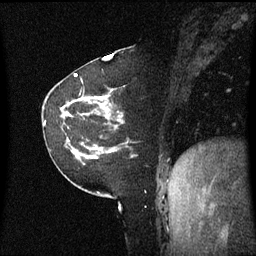
Breast MRI (dynamic contrast-enhanced), one sagittal slice; position 20 of 60 along the scan axis; dynamic contrast-enhanced series, image 2 of 3 at this slice position (ordered by acquisition); 1.5 T; TE 4.2 ms, TR 8.4 ms; 256 × 256 image matrix, field of view 220 × 220 mm. Female patient, age 60 years. Case-level facts recorded for this patient, not image findings: setting: breast cancer imaged before/during neoadjuvant chemotherapy; receptor status: triple-negative.
Annotated regions visible in this slice (semi-automatic segmentation, software-assisted and operator-edited):
- analysis volume of interest (the breast-tissue region the enhancement analysis was run in; not a lesion): bounding box (x1, y1, x2, y2) in pixels: (62, 98, 127, 161)
- tumour enhancement mask (voxels above the 70 % enhancement threshold inside the analysis volume of interest): (80, 98, 82, 101)